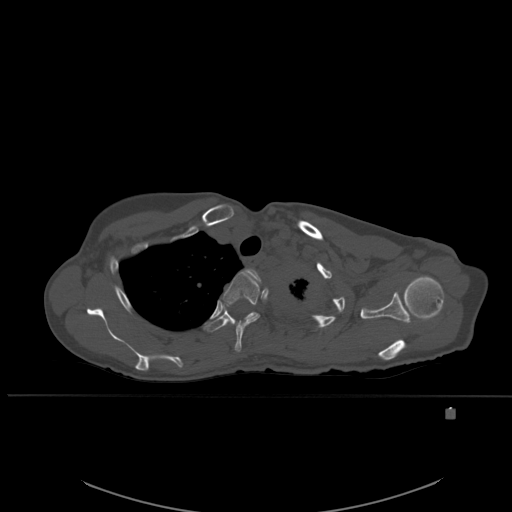
CT including the spine, one axial slice. Position 421 of 537 along the scan axis. Bone window (W 1800 / L 400 HU). 1.5 mm slice thickness. 512 × 512 image matrix. Female patient, age 45 years. From the clinical record (not read from this slice): primary cancer: lung.
Outlined on this slice (semi-automatically segmented with operator editing):
- T2 vertebra: bounding box [x1, y1, x2, y2] px = [247, 269, 261, 287]
- T3 vertebra: [223, 271, 260, 352]
- T4 vertebra: [206, 302, 256, 332]